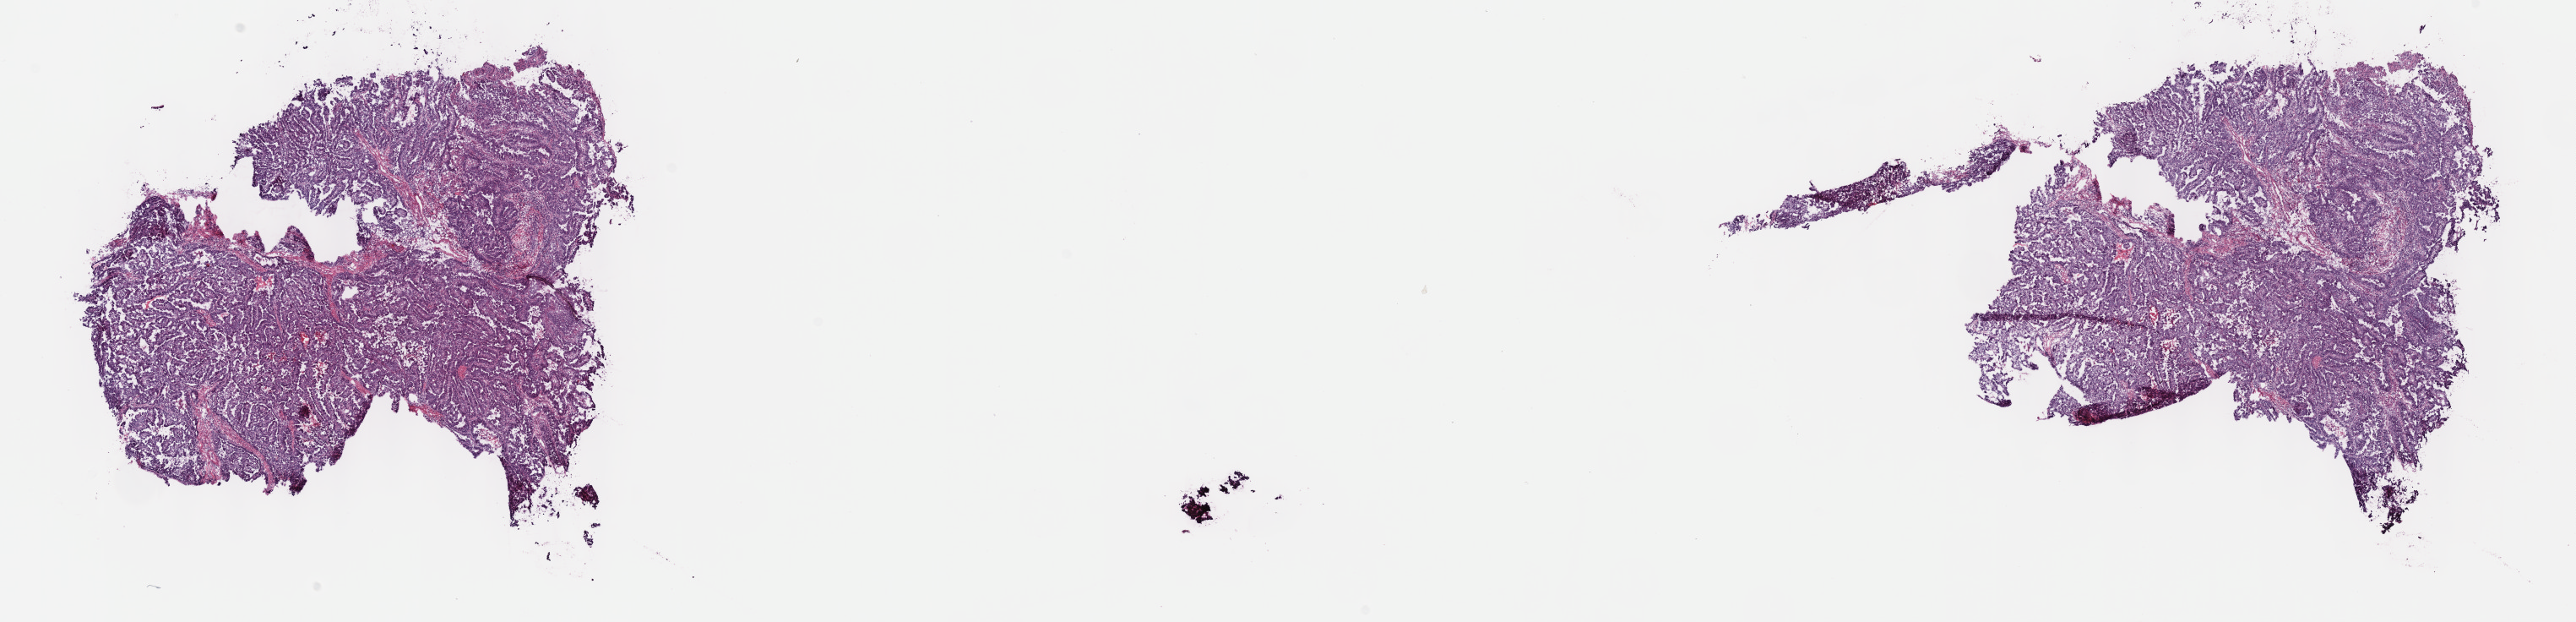
H&E-stained whole-slide image — whole scanned area (about 24.7 x 6.0 mm) shown as a low-resolution overview, frozen section, sample: primary tumour, pancreas. Male patient; age at initial diagnosis 72 years. Histologic grade: GX (grade cannot be assessed). Composition of this section per pathologist review: tumour cells 70%, tumour nuclei 70%, normal cells 0%, stromal cells 25%, necrosis 5%. Infiltration values recorded for this section: lymphocyte infiltration 40%, monocyte infiltration 20%, neutrophil infiltration 20%.
Histologic diagnosis: Infiltrating duct carcinoma, NOS (head of pancreas). AJCC pathologic stage: IIB (7th edition).